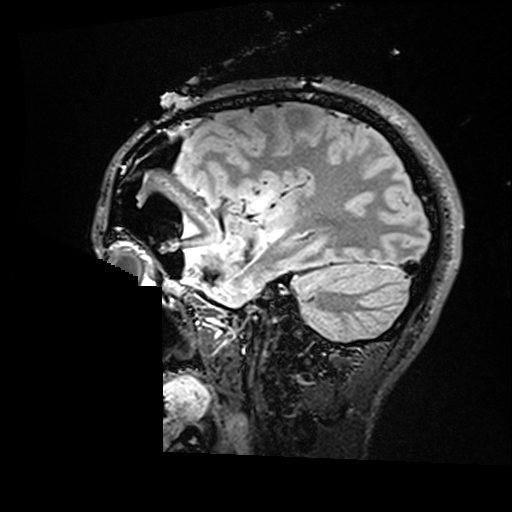
Brain MRI from a brain-tumour surgery series, one sagittal slice. Slice 121 of 176 in the series (ordered by position). T2 FLAIR. 1 mm slice thickness. 512 × 512 image matrix, field of view 250 × 250 mm. Case-level facts recorded for this patient, not image findings: histopathology: Astrocytoma; WHO grade: 2; IDH mutation: yes; tumour location: Right Insular.
Outlined on this slice (outlined manually by an expert reader):
- residual tumour: bounding box [x1, y1, x2, y2] px = [256, 190, 275, 209]